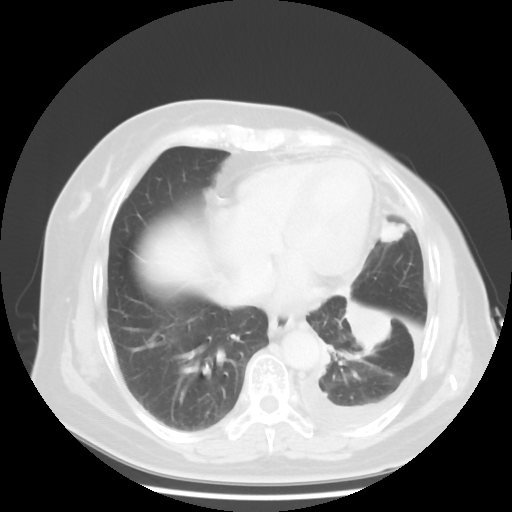
Chest CT, one axial slice. Slice 15 of 48 in the series (ordered by position). Lung window (W 1500 / L -600 HU). 512 × 512 image matrix, field of view 360 × 360 mm. Patient: female, 63 years. Case-level facts recorded for this patient, not image findings: clinical TNM (as recorded): T2 N0 M1.
Structures marked on this image (bounding box drawn by a radiologist):
- lung tumour (recorded histology: adenocarcinoma): bounding box [x1, y1, x2, y2] px = [334, 295, 404, 365]